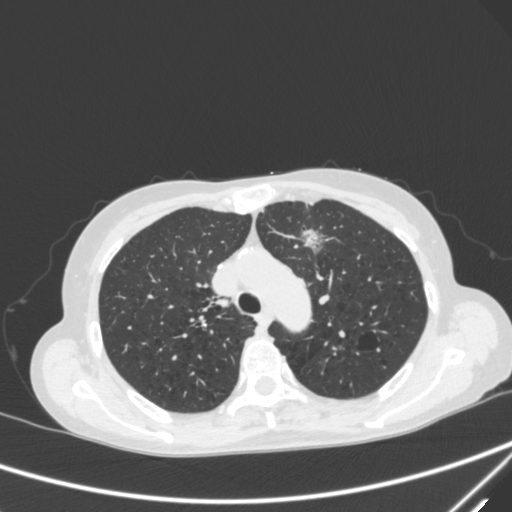
Chest CT, one axial slice. Position 222 of 300 along the scan axis. Lung window (W 1500 / L -600 HU). 512 × 512 image matrix. Female patient, age 71 years. Case-level facts recorded for this patient, not image findings: clinical TNM (as recorded): T1c N0 M0; histopathological grade: G2-3.
Annotated regions visible in this slice (bounding box drawn by a radiologist):
- lung tumour (recorded histology: adenocarcinoma): bounding box [x1, y1, x2, y2] px = [295, 223, 328, 263]